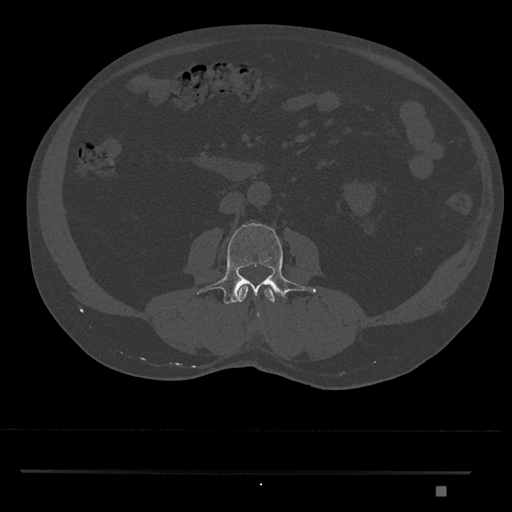
CT including the spine, one axial slice. Slice 695 of 1134 in the series (ordered by position). Reconstruction kernel Br40s/3. Bone window (W 1800 / L 400 HU). 512 × 512 image matrix. Patient: male, 65 years. Case-level facts recorded for this patient, not image findings: primary cancer: prostate.
Structures marked on this image (semi-automatic segmentation, software-assisted and operator-edited):
- L2 vertebra: bounding box <237,286,275,303> (left, top, right, bottom; pixels)
- L3 vertebra: <197,223,316,317>